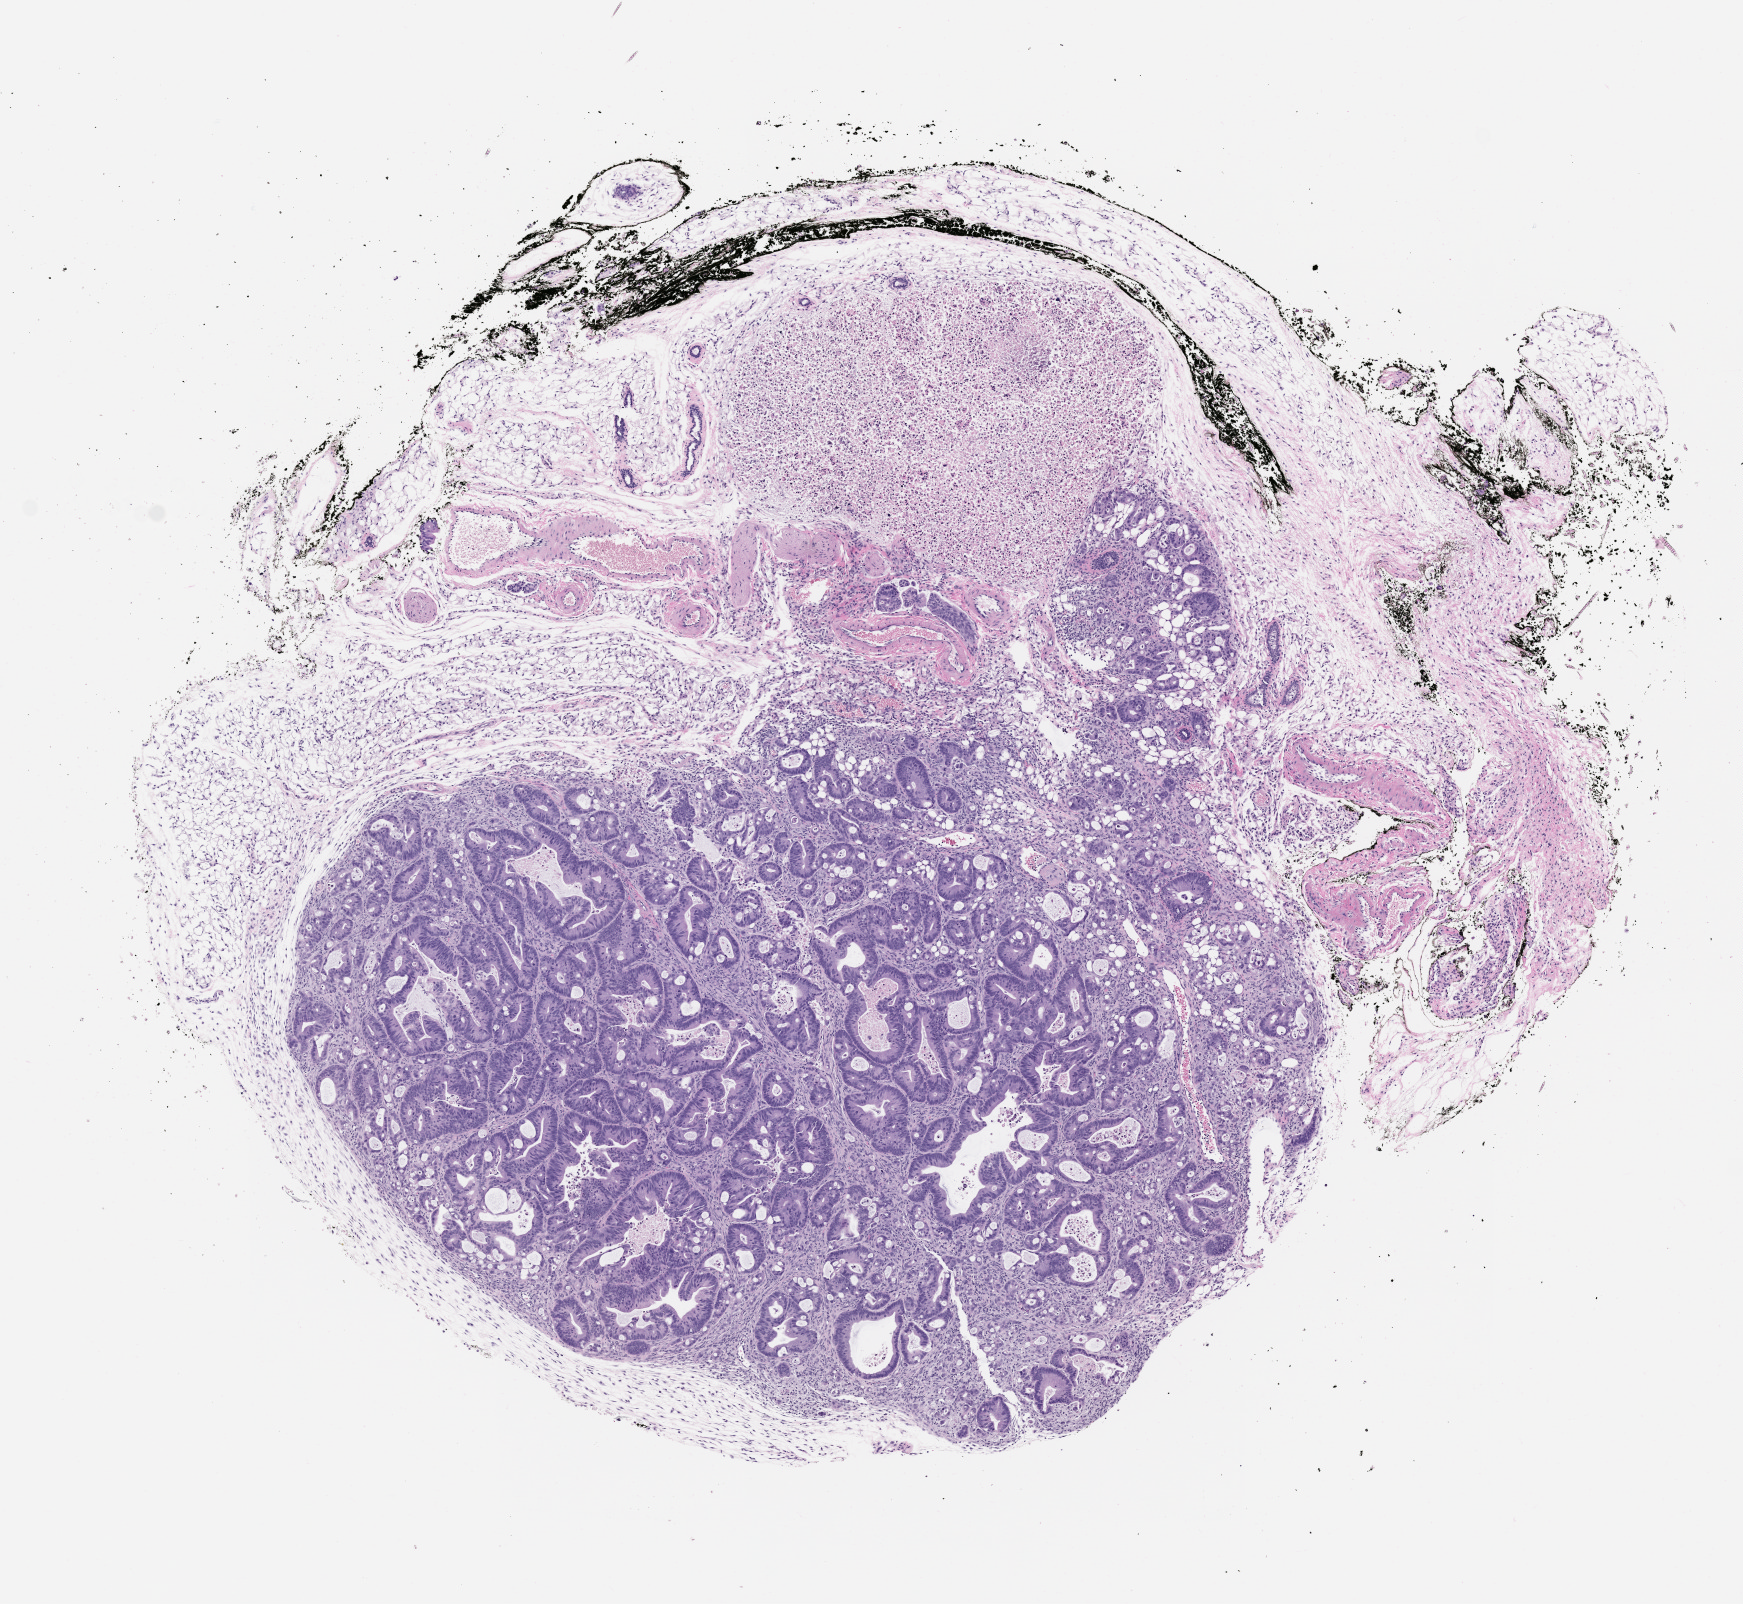
Whole-slide image, haematoxylin and eosin: patient-derived xenograft (human tumor grown in a mouse), passage 1, shown as a low-resolution overview of the whole scanned area (about 7.0 x 6.5 mm). Formalin-fixed paraffin-embedded section. Originating tumor site category: rectum.
Originating patient diagnosis: Rectal Adenocarcinoma.